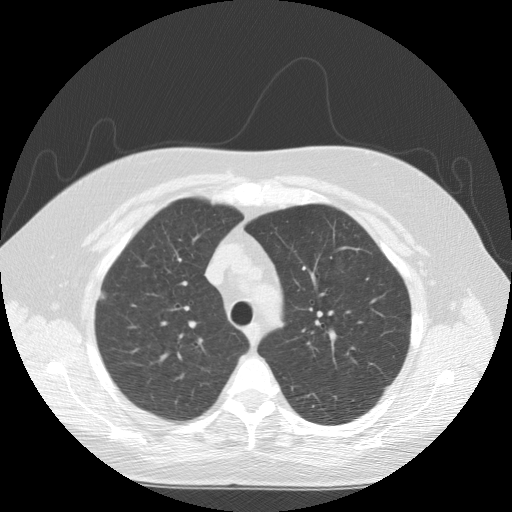
Low-dose screening chest CT, one axial slice. Reconstruction kernel STANDARD. Lung window (W 1500 / L -600 HU). 2.5 mm slice thickness. 512 × 512 image matrix.
Outlined on this slice (expert manual segmentation):
- lesion 1 (tumor, upper lobe of right lung): box from (x=100, y=293) to (x=104, y=298) px